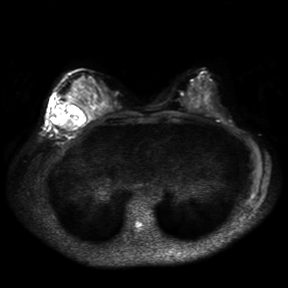
Breast MRI, one axial slice; slice 16 of 30 in the series (ordered by position); diffusion-weighted series; image 2 of 4 stored at this slice position (different b-values; order by instance number); 3 T; 4 mm slice thickness; 288 × 288 image matrix, field of view 360 × 360 mm. Female patient.
Structures marked on this image (outlined manually by an expert reader):
- tumour on diffusion-weighted imaging: bounding box [x1, y1, x2, y2] px = [56, 103, 72, 128]